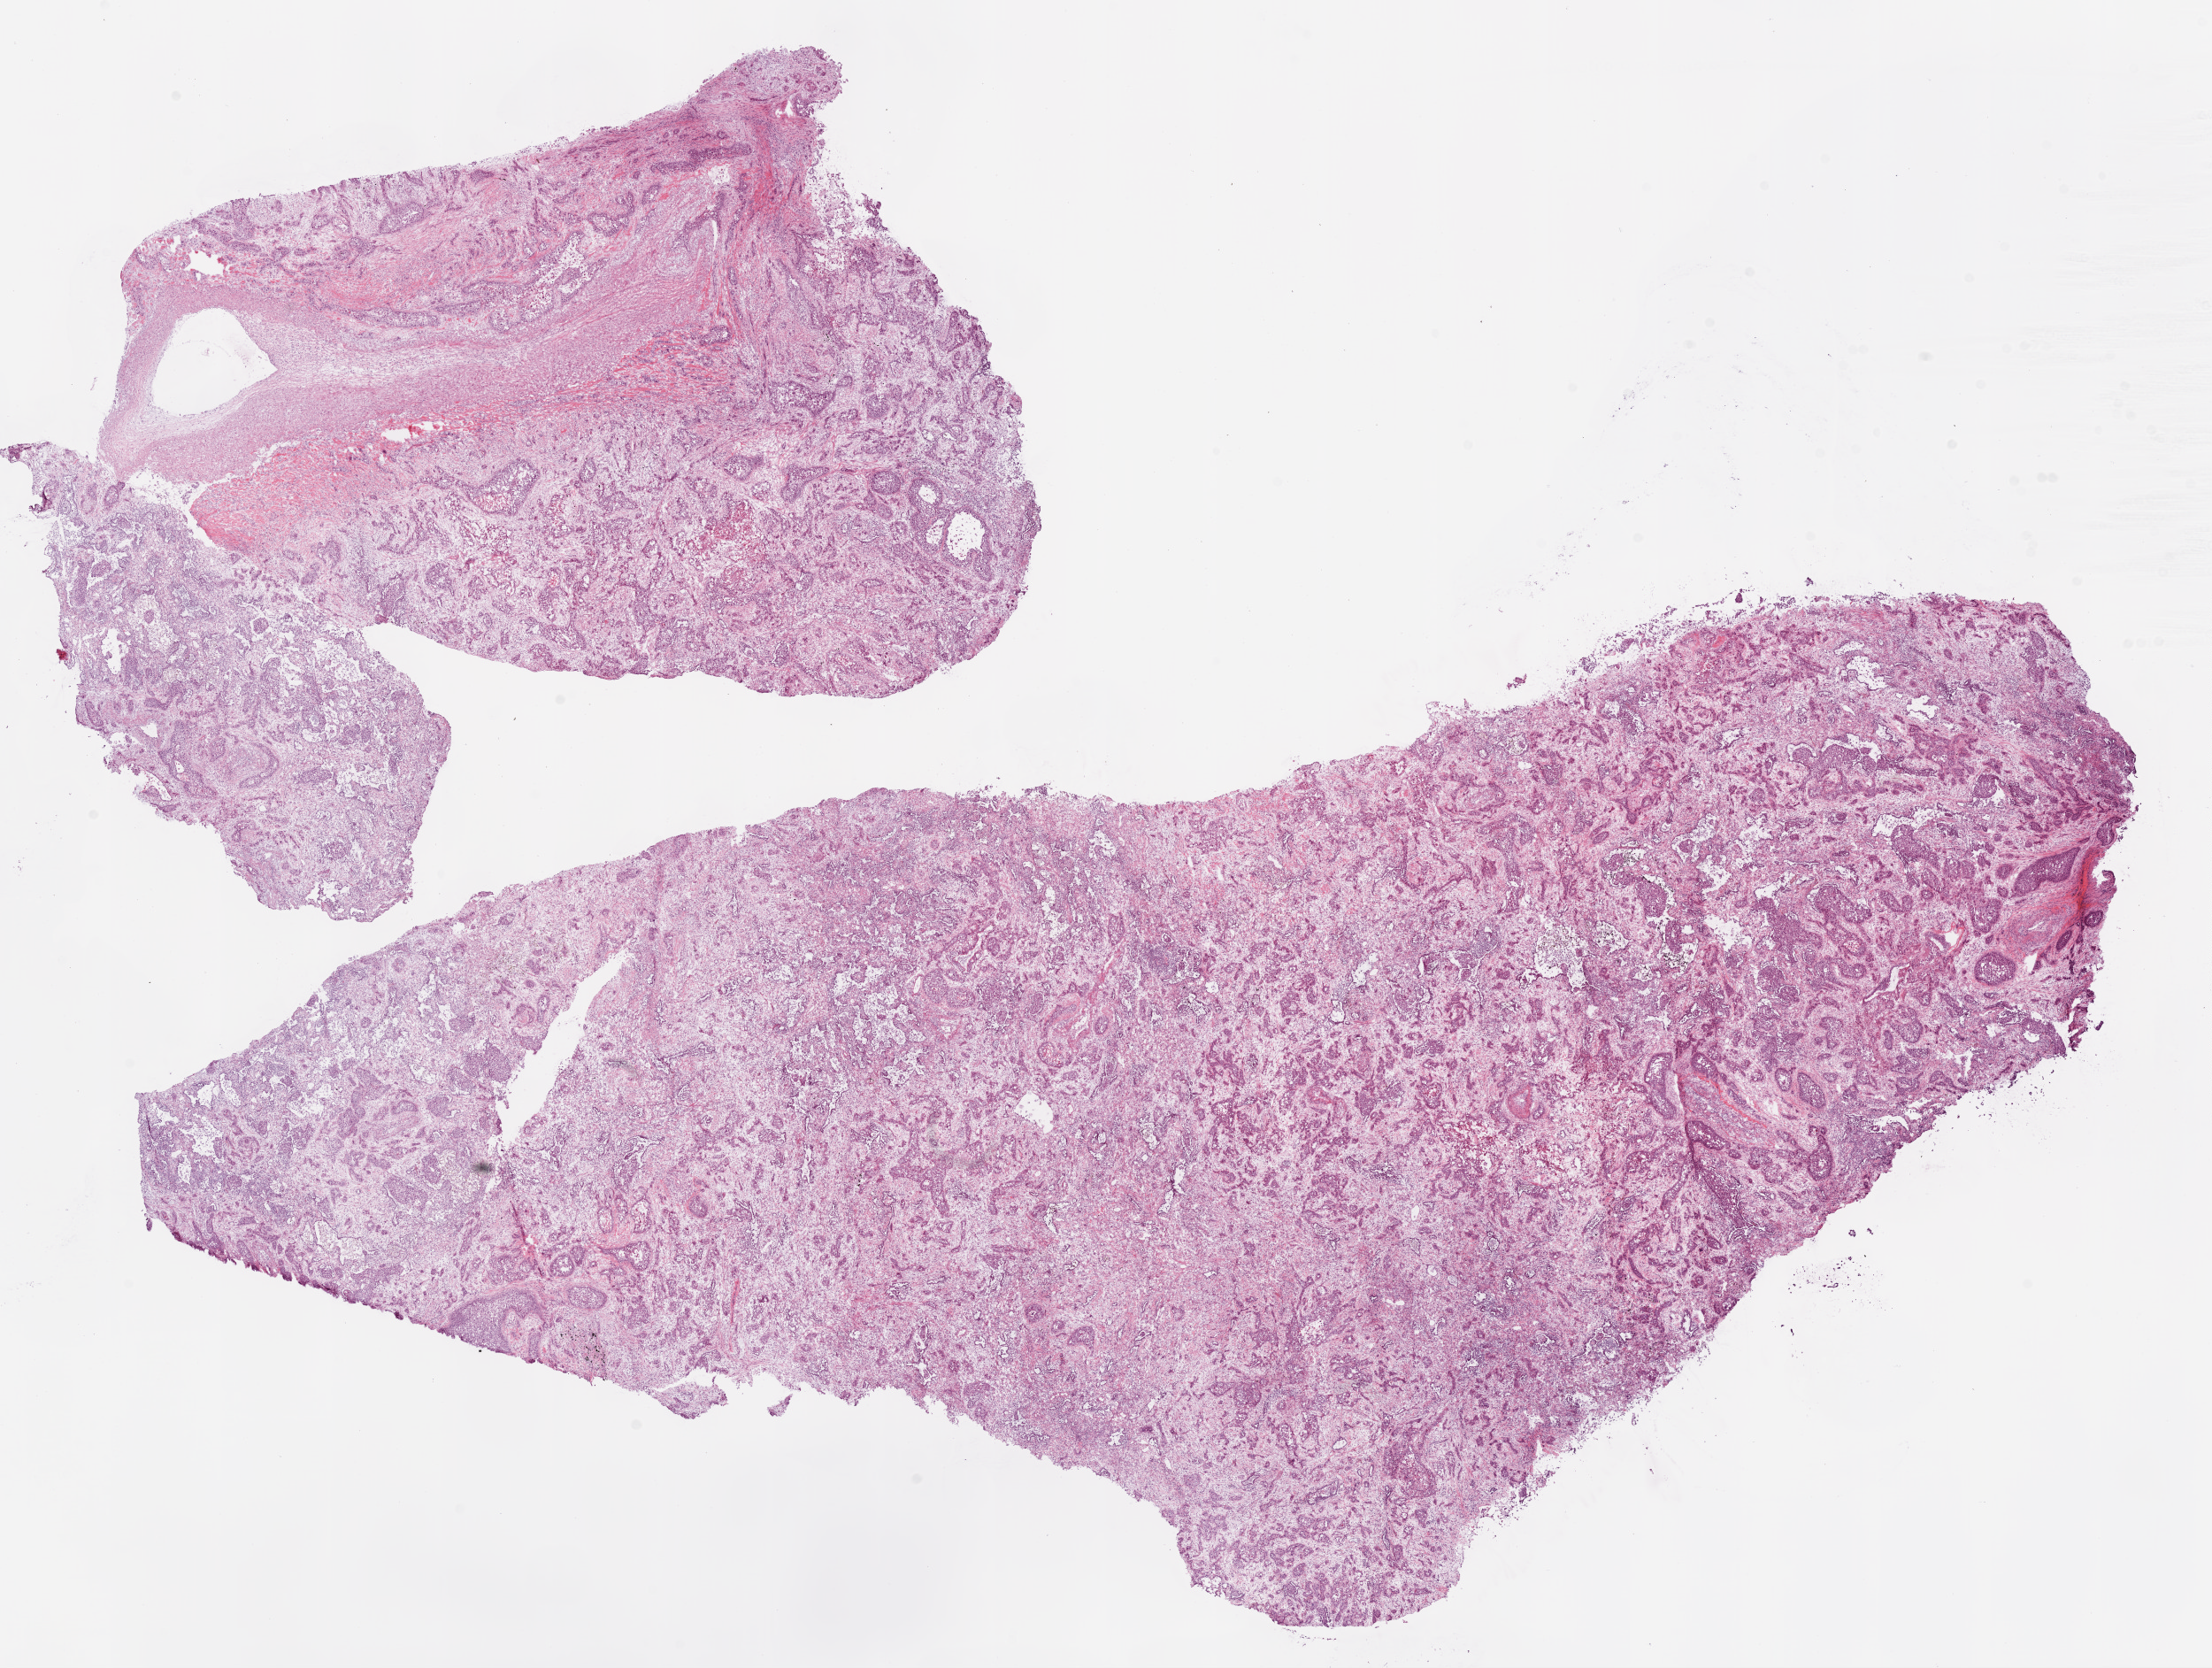
H&E whole-slide image, shown as a low-resolution overview of the whole scanned area (about 20.1 x 15.1 mm). Frozen section from the top of the tissue portion. Sample: primary tumour, lung. Male patient; age at initial diagnosis 76 years. Composition of this section per pathologist review: tumour cells 65%, tumour nuclei 70%, normal cells 0%, stromal cells 30%, necrosis 5%.
AJCC pathologic stage: IIA. Histologic diagnosis: Squamous cell carcinoma, NOS (upper lobe, lung).